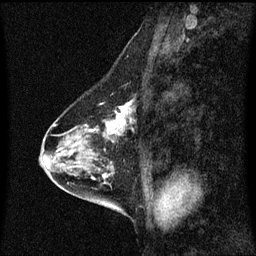
Breast MRI (dynamic contrast-enhanced), one sagittal slice. Dynamic contrast-enhanced series, image 2 of 3 at this slice position (ordered by acquisition). 1.5 T. TE 4.2 ms, TR 8.4 ms. 2 mm slice thickness. 256 × 256 image matrix, field of view 200 × 200 mm. Patient: female, 58 years.
Structures marked on this image (semi-automatically segmented with operator editing):
- analysis volume of interest (the breast-tissue region the enhancement analysis was run in; not a lesion): bounding box <86,92,137,143> (left, top, right, bottom; pixels)
- tumour enhancement mask (voxels above the 70 % enhancement threshold inside the analysis volume of interest): <86,100,134,143>